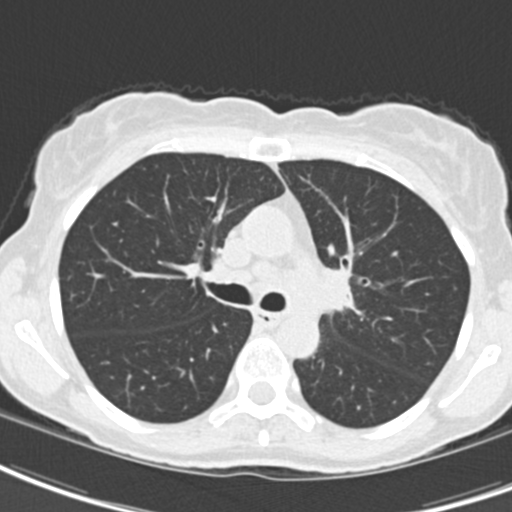
Low-dose screening chest CT, one axial slice; 120 kVp; lung window (W 1500 / L -600 HU); 512 × 512 image matrix, field of view 279 × 279 mm.
Outlined on this slice (outlined manually by an expert reader):
- lesion 2 (tumor, hilum of left lung): bounding box [x1, y1, x2, y2] px = [320, 267, 345, 311]